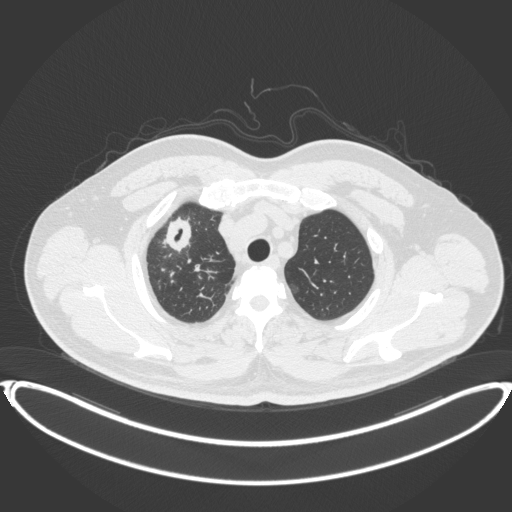
Chest CT, one axial slice. Slice 328 of 399 in the series (ordered by position). 120 kVp. Lung window (W 1500 / L -600 HU). 1 mm slice thickness. 512 × 512 image matrix, field of view 445 × 445 mm. Male patient, age 53 years. Case-level facts recorded for this patient, not image findings: clinical TNM (as recorded): T2a N0 M0.
Annotated regions visible in this slice (bounding box drawn by a radiologist):
- lung tumour (recorded histology: adenocarcinoma): box from (x=159, y=211) to (x=196, y=260) px